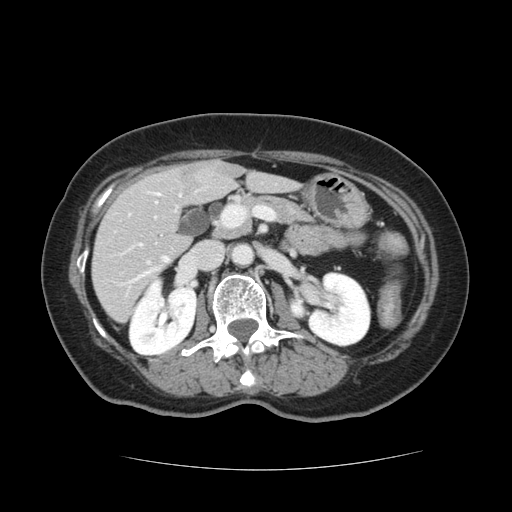
Contrast-enhanced abdominal CT, one axial slice. Slice 53 of 128 in the series (ordered by position). 120 kVp. Soft-tissue window (W 400 / L 40 HU). 2.5 mm slice thickness. 512 × 512 image matrix. Female patient, age 67 years. Case-level facts recorded for this patient, not image findings: diagnosis: colorectal cancer liver metastases, imaged before liver resection; multiple liver metastases: yes; largest metastasis: 3 cm.
Outlined on this slice (outlined manually by an expert reader):
- hepatic veins: bounding box [x1, y1, x2, y2] px = [117, 255, 170, 288]
- liver: [94, 161, 294, 322]
- planned liver remnant (the part of the liver to remain after resection): [94, 172, 295, 321]
- portal vein (with intrahepatic branches): [112, 208, 242, 264]